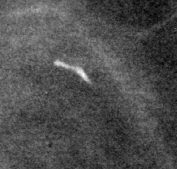
Crop from a digitized film mammogram around one marked abnormality, left breast, CC view.
Calcifications, distribution regional; BI-RADS assessment category 2; subtlety rating 3 on a 1 (subtle) to 5 (obvious) scale; benign without callback (not worked up further).